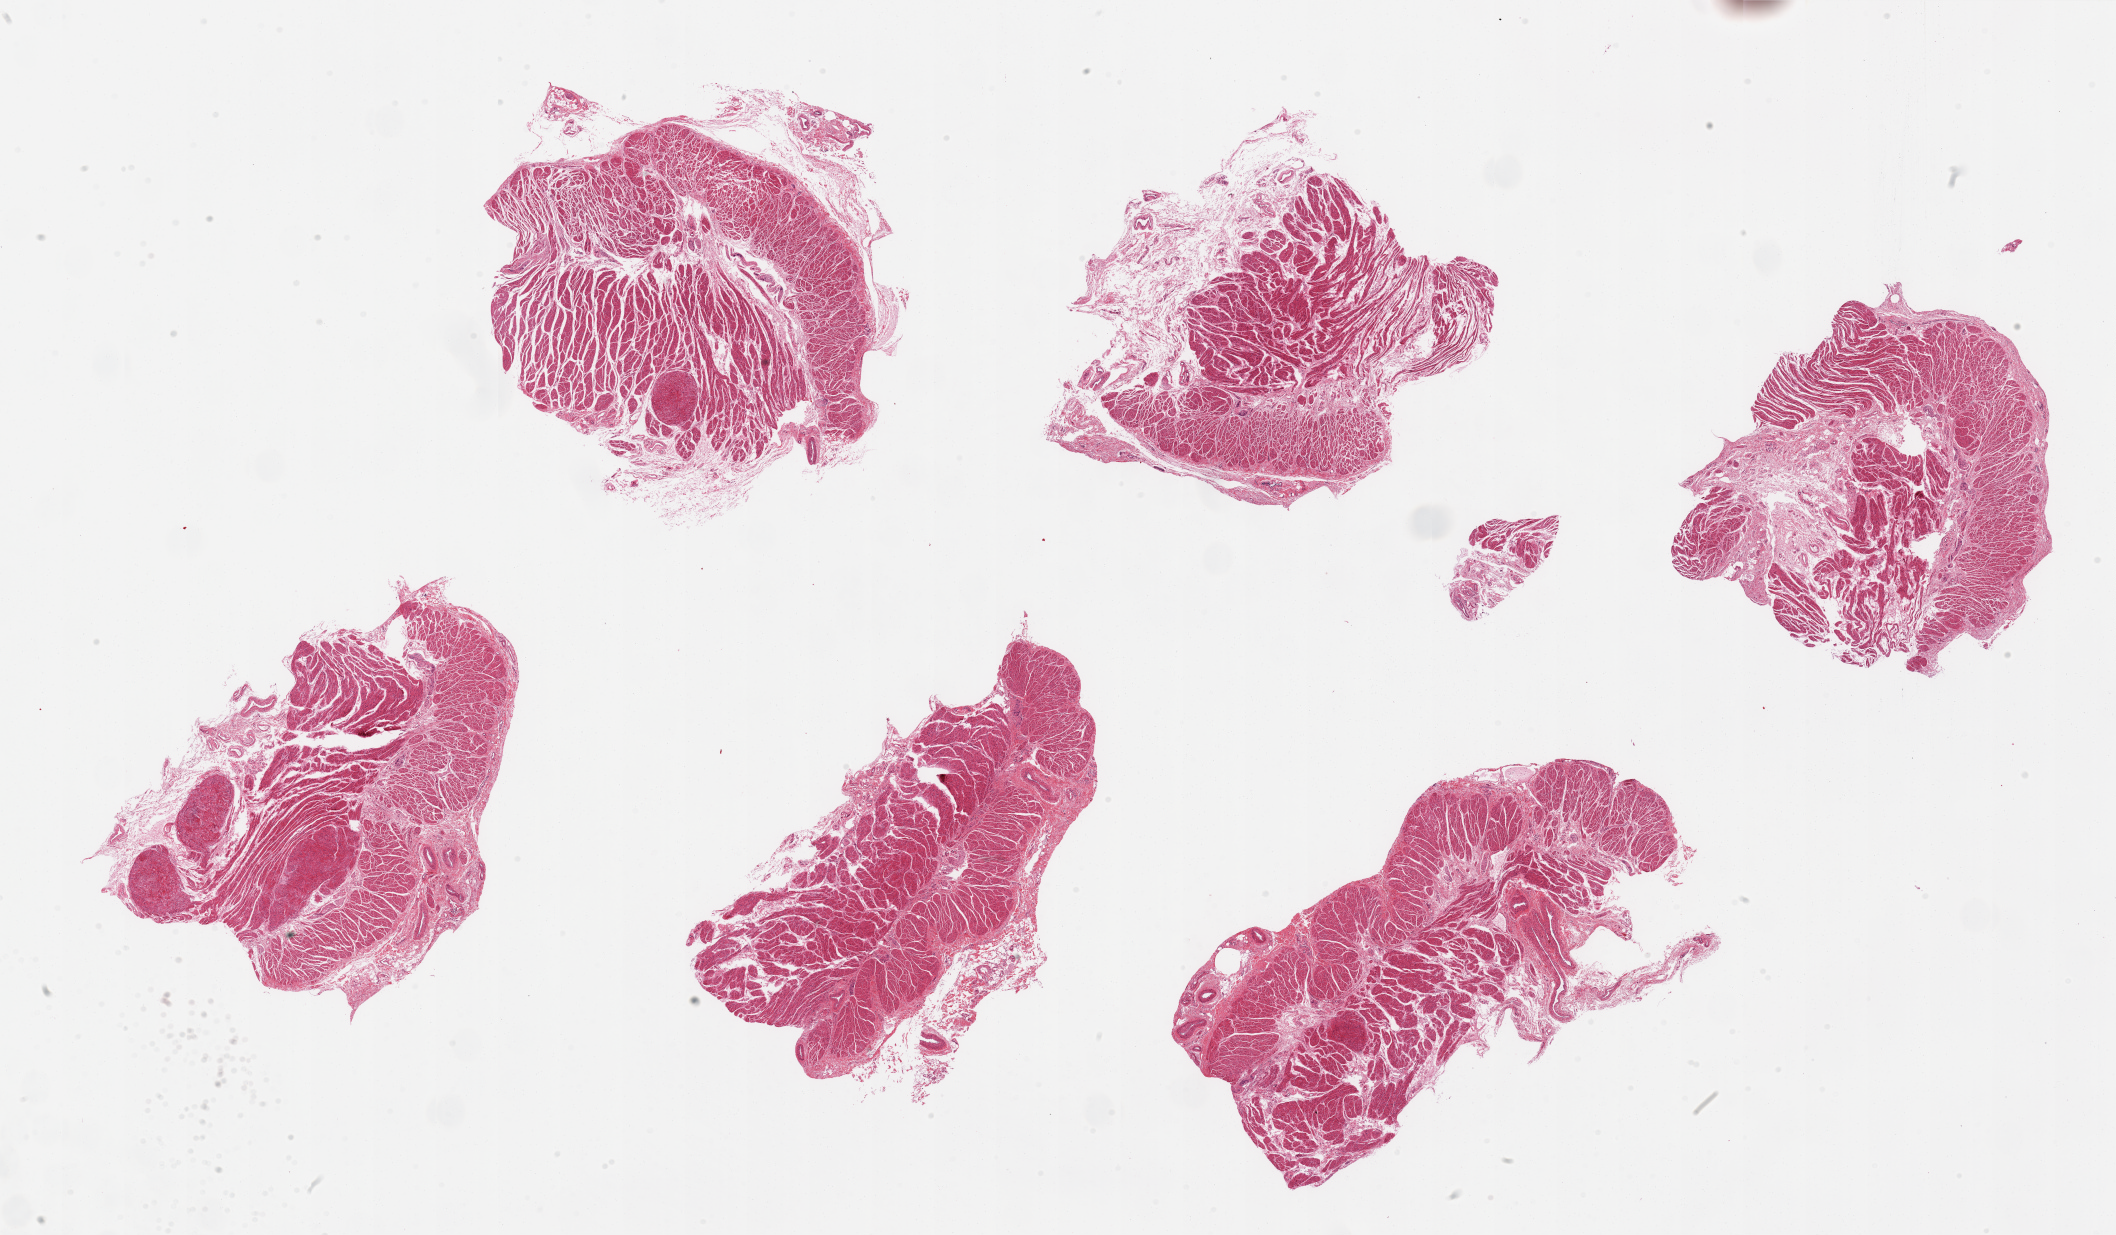
Digitized hematoxylin and eosin (H&E)-stained section, low-resolution overview of the scanned area, about 33.5 x 19.5 mm; PAXgene-fixed, paraffin-embedded tissue; sampled site (target tissue): gastroesophageal junction; donor tissue sample. Female donor.
Review note (as recorded): 6 pieces.